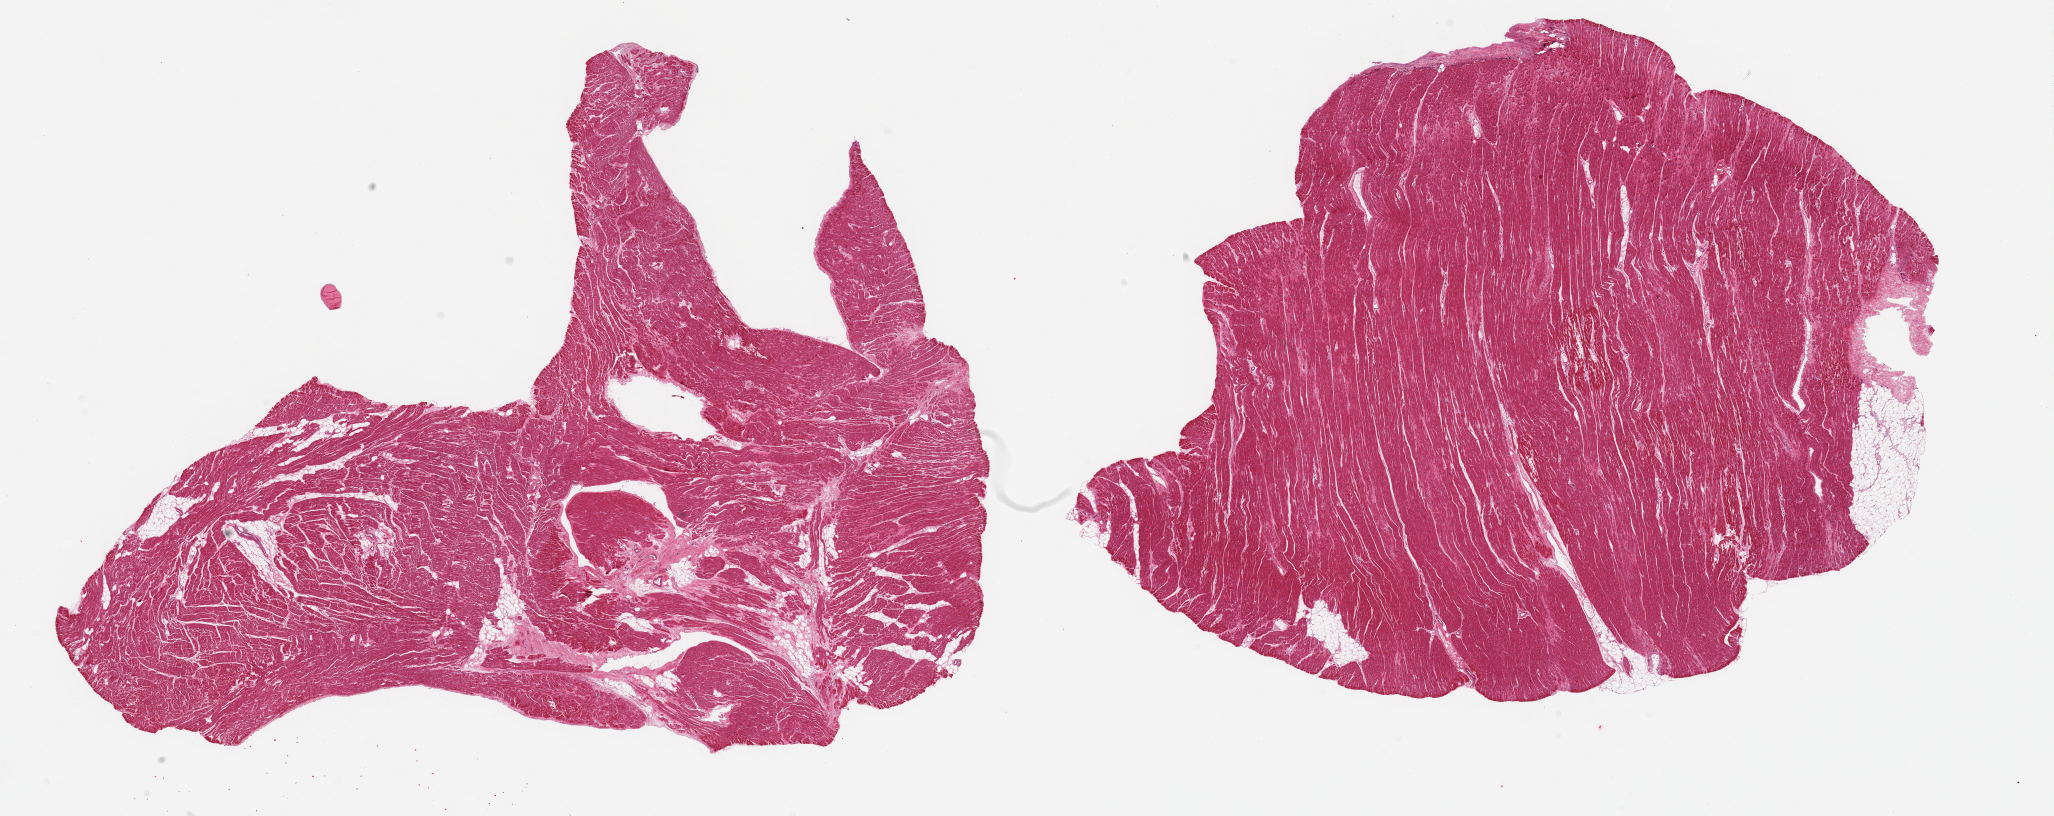
Digitized H&E-stained section, low-resolution overview of the scanned area, about 32.5 x 12.9 mm (acquisition: 20x scan); PAXgene-fixed, paraffin-embedded tissue; target tissue: auricular appendage; donor tissue sample. Donor sex: male.
* reviewer comment on this tissue sample: 2 pieces, 15x11 & 14x11mm; Good specimen